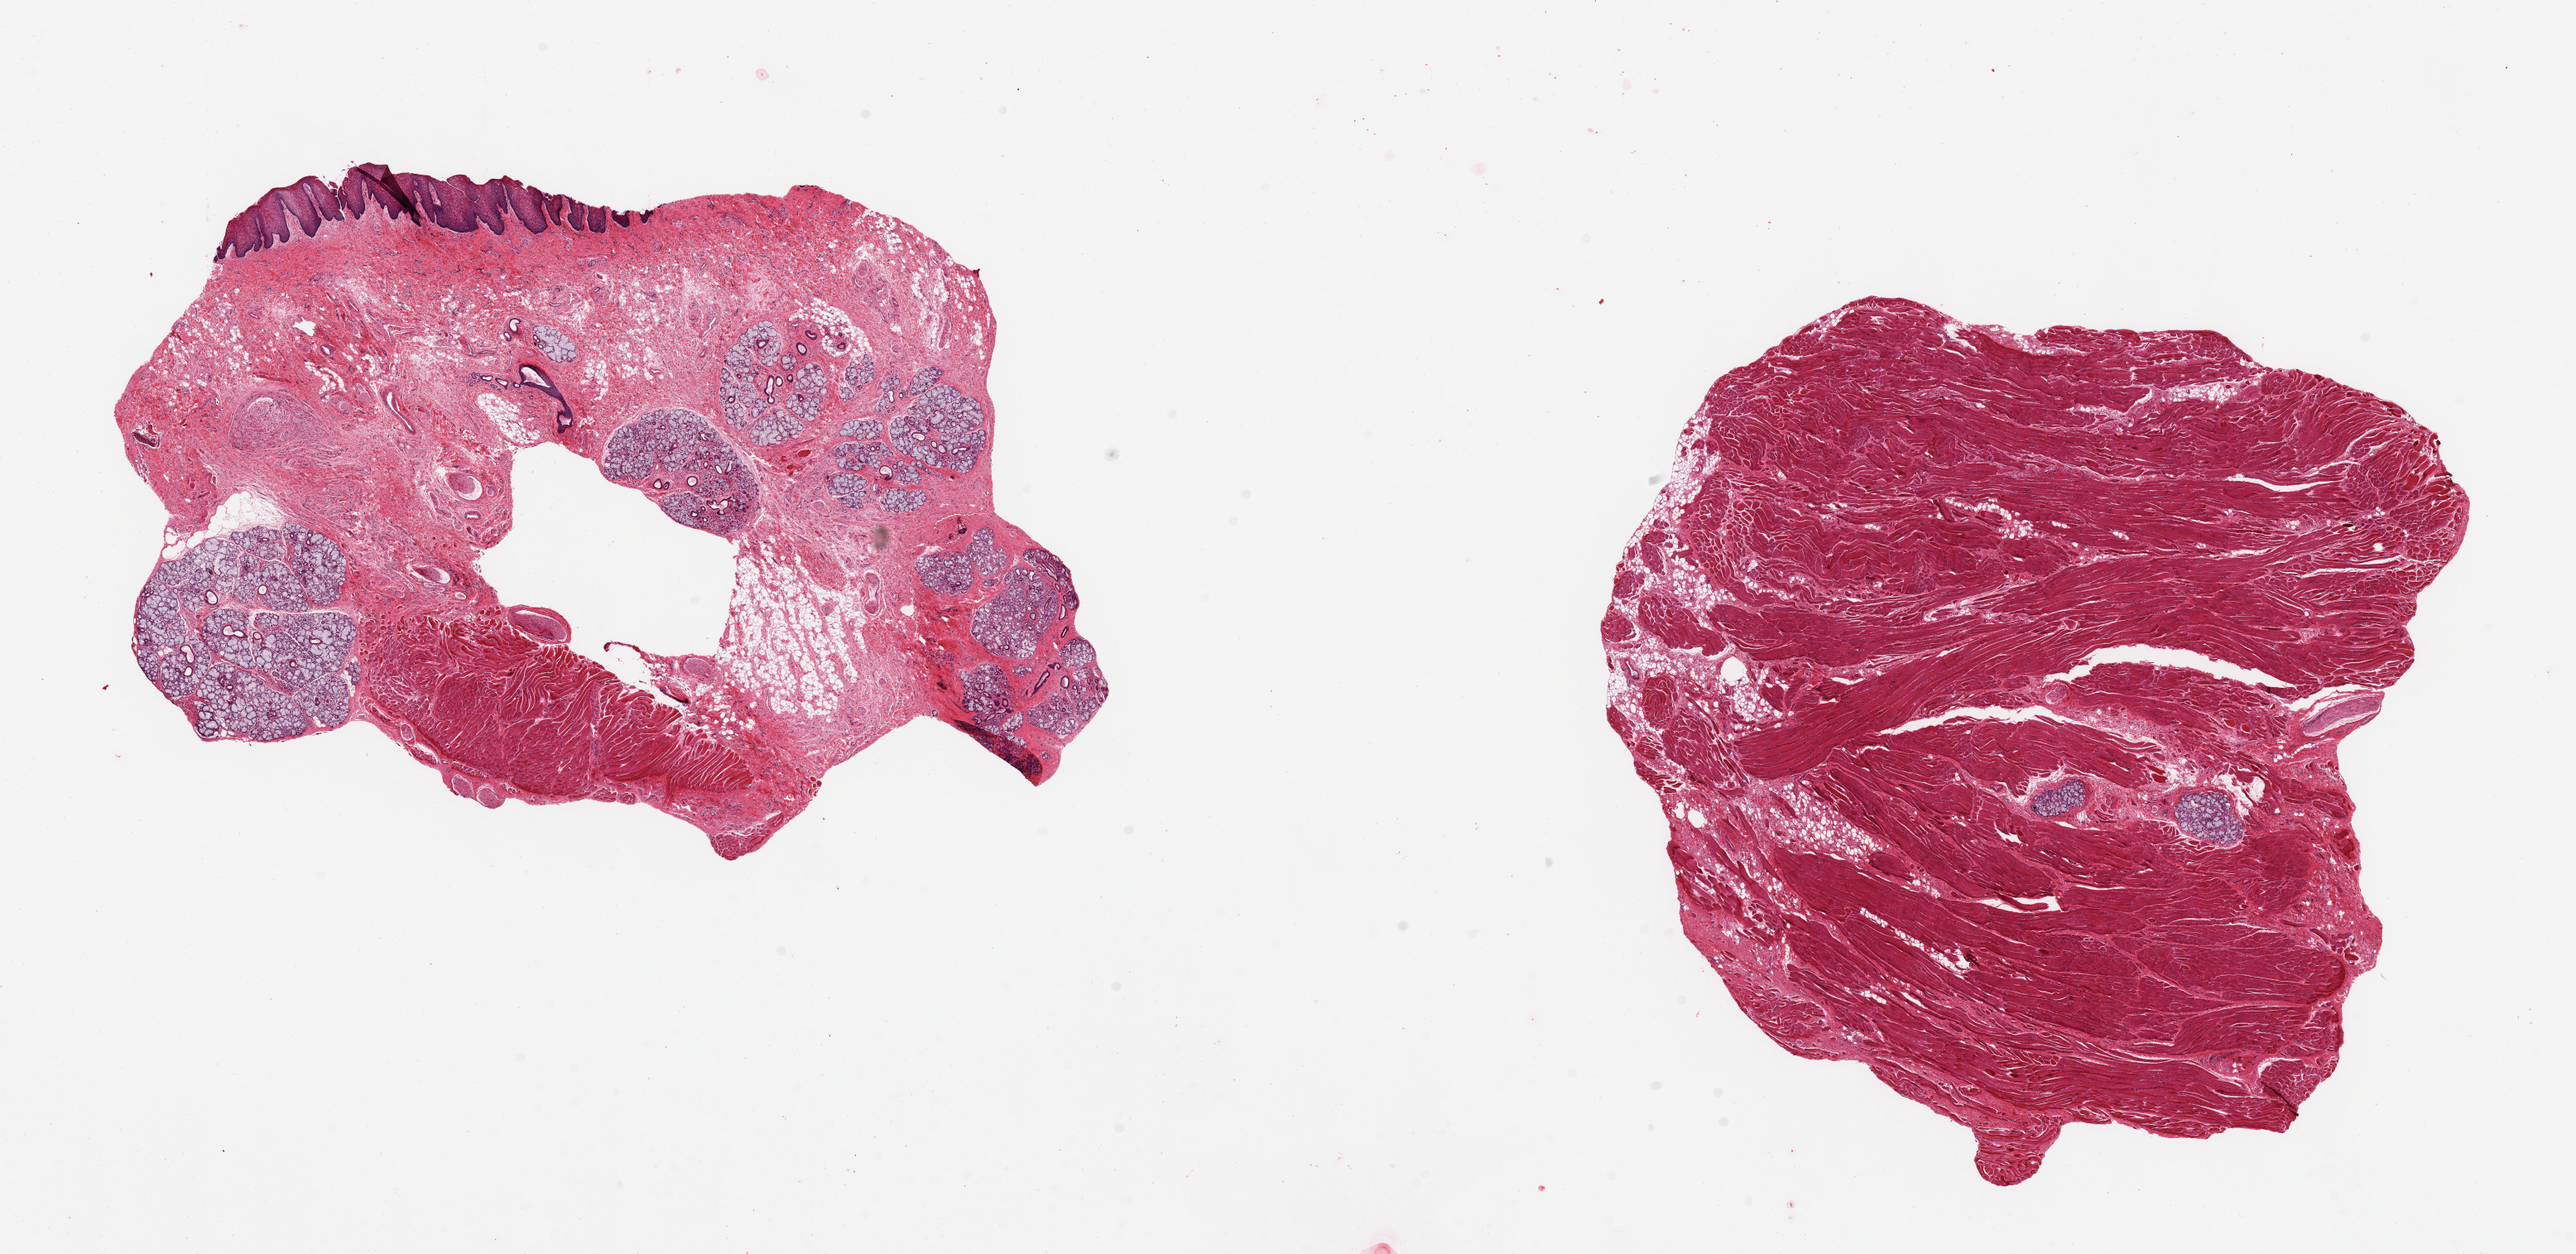
Digitized haematoxylin and eosin-stained section, brightfield, low-resolution overview of the scanned area, about 24.6 x 12.0 mm. Male donor.
Specimen: PAXgene-fixed, paraffin-embedded tissue; section of minor salivary gland (target tissue); tissue donor sample.